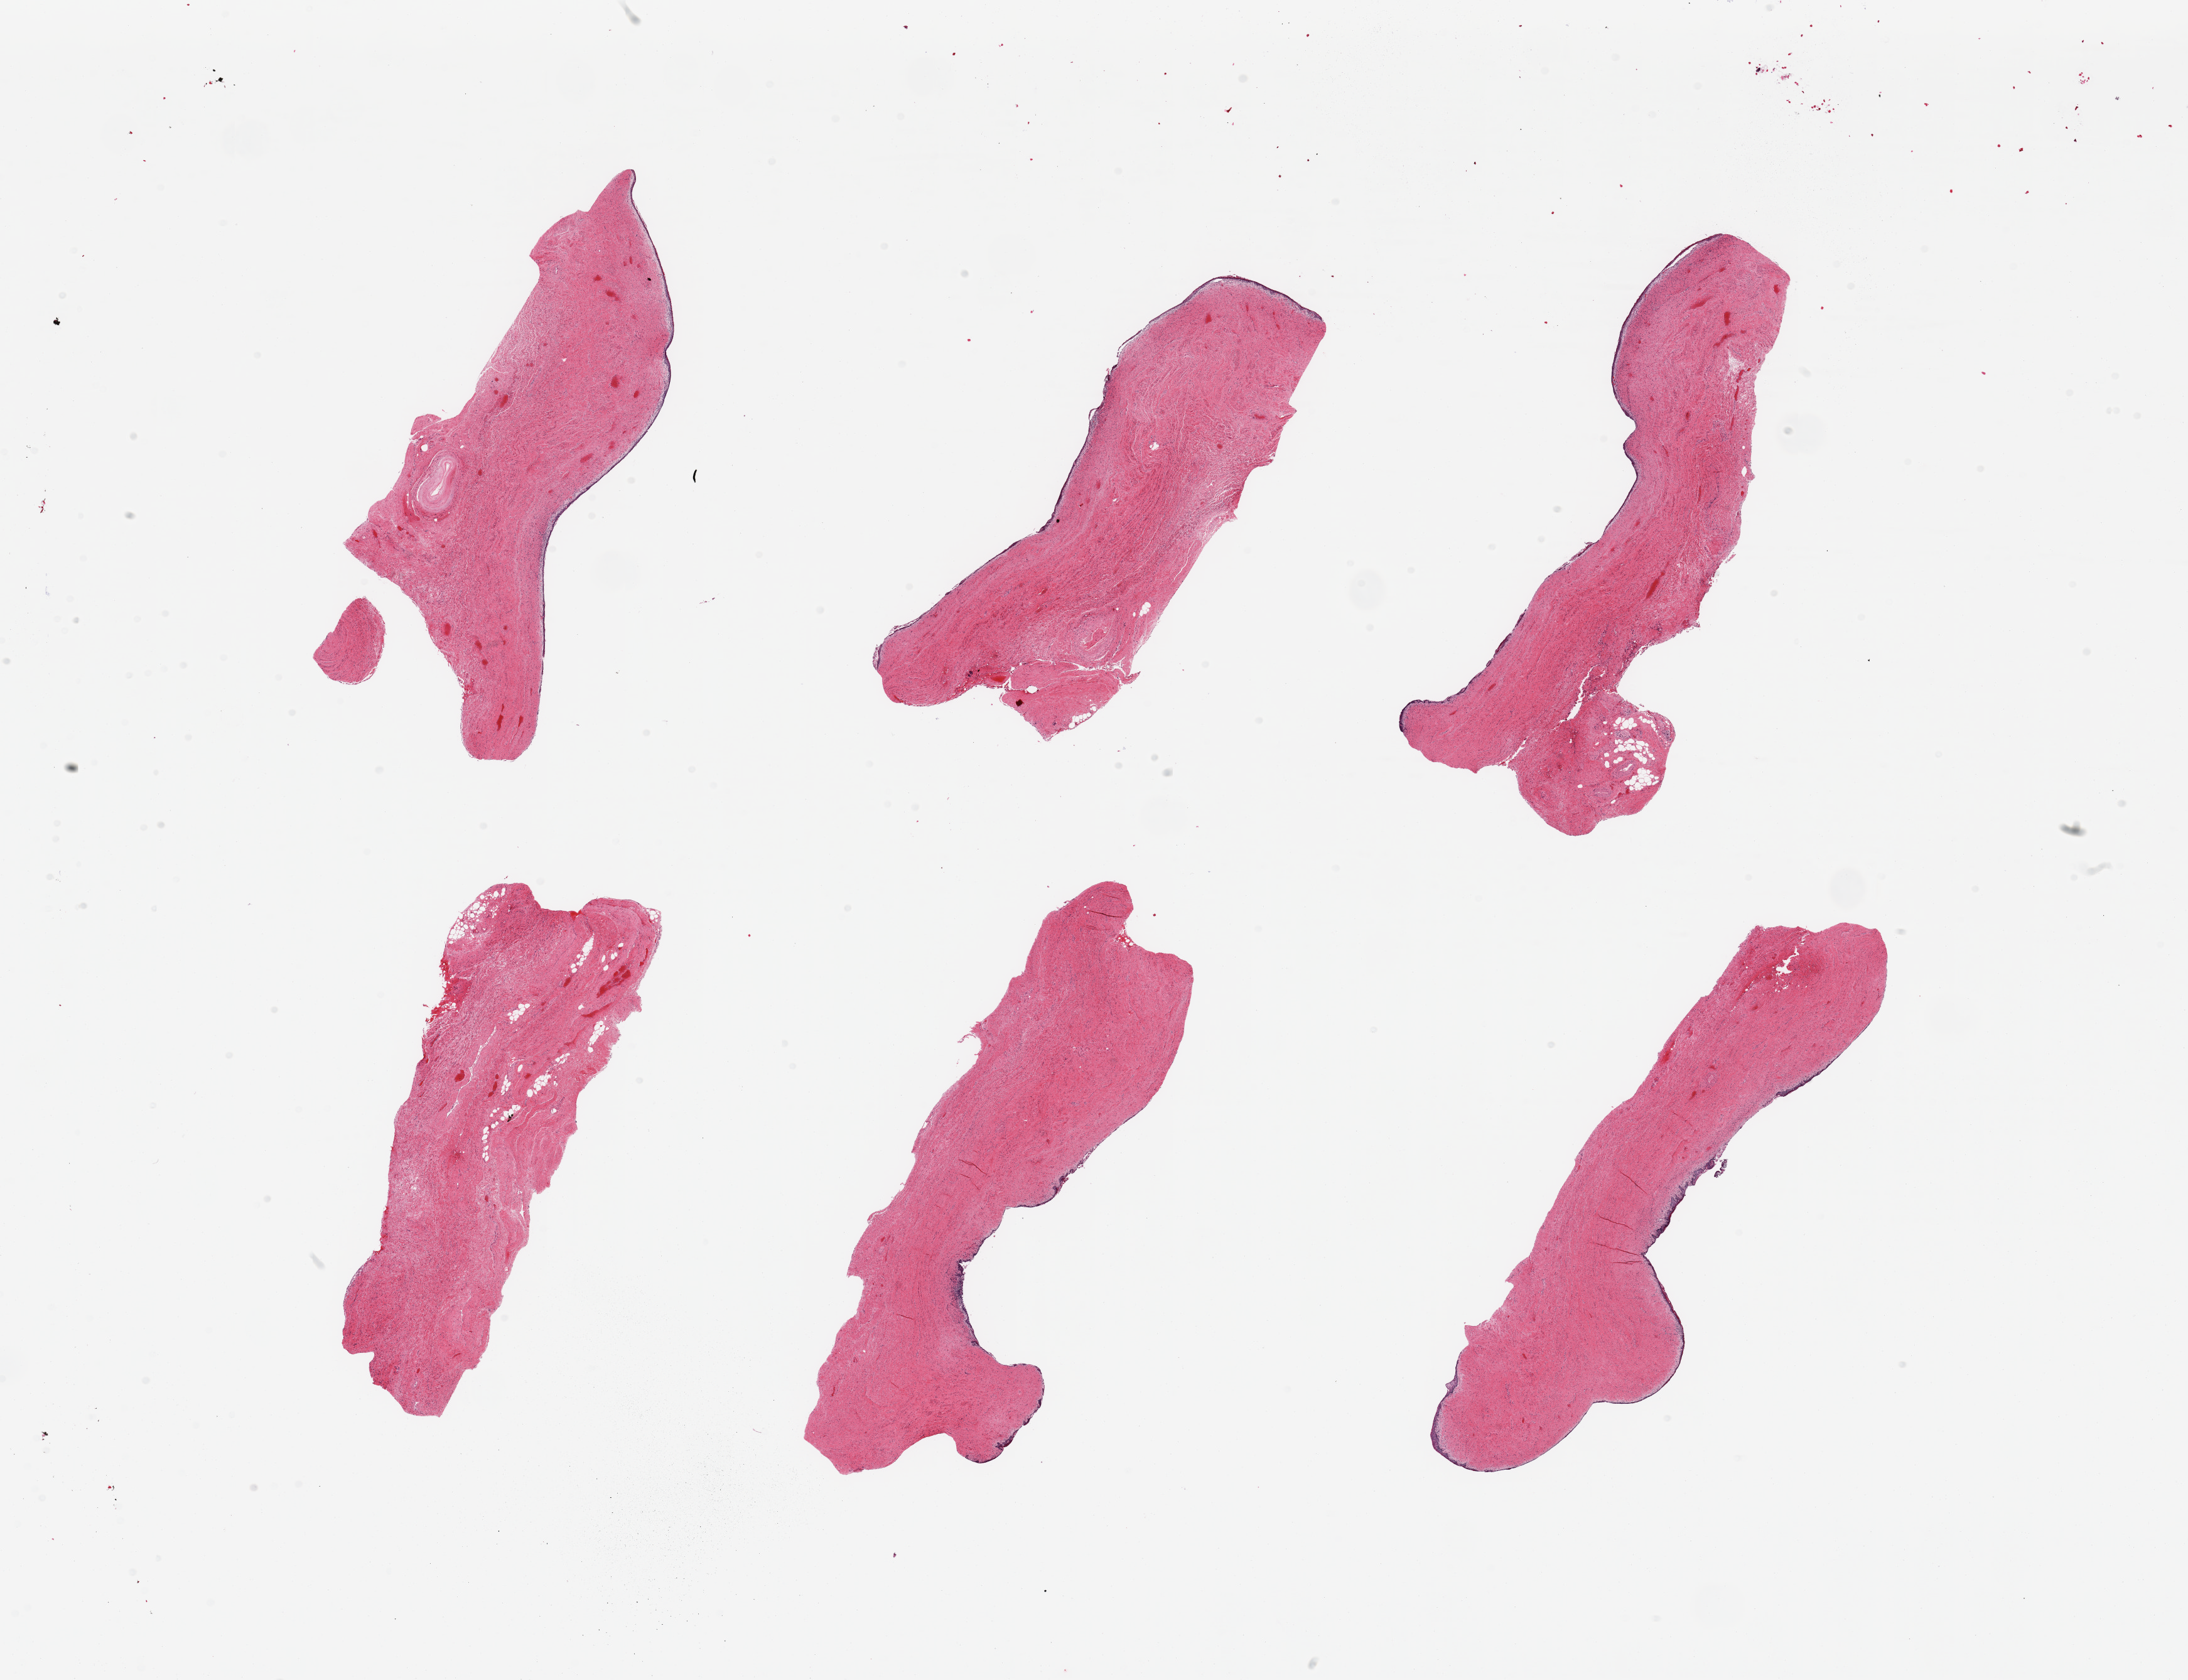
Digitized H&E-stained section — shown as a low-resolution overview of the whole scanned area (about 27.6 x 21.2 mm, slide scanned at 20x); PAXgene-fixed, paraffin-embedded tissue; target tissue: vagina; donor tissue sample. Donor: female.
Review note (as recorded): 6 pieces, squamous mucosa partially sloughing, up to ~50 microns.